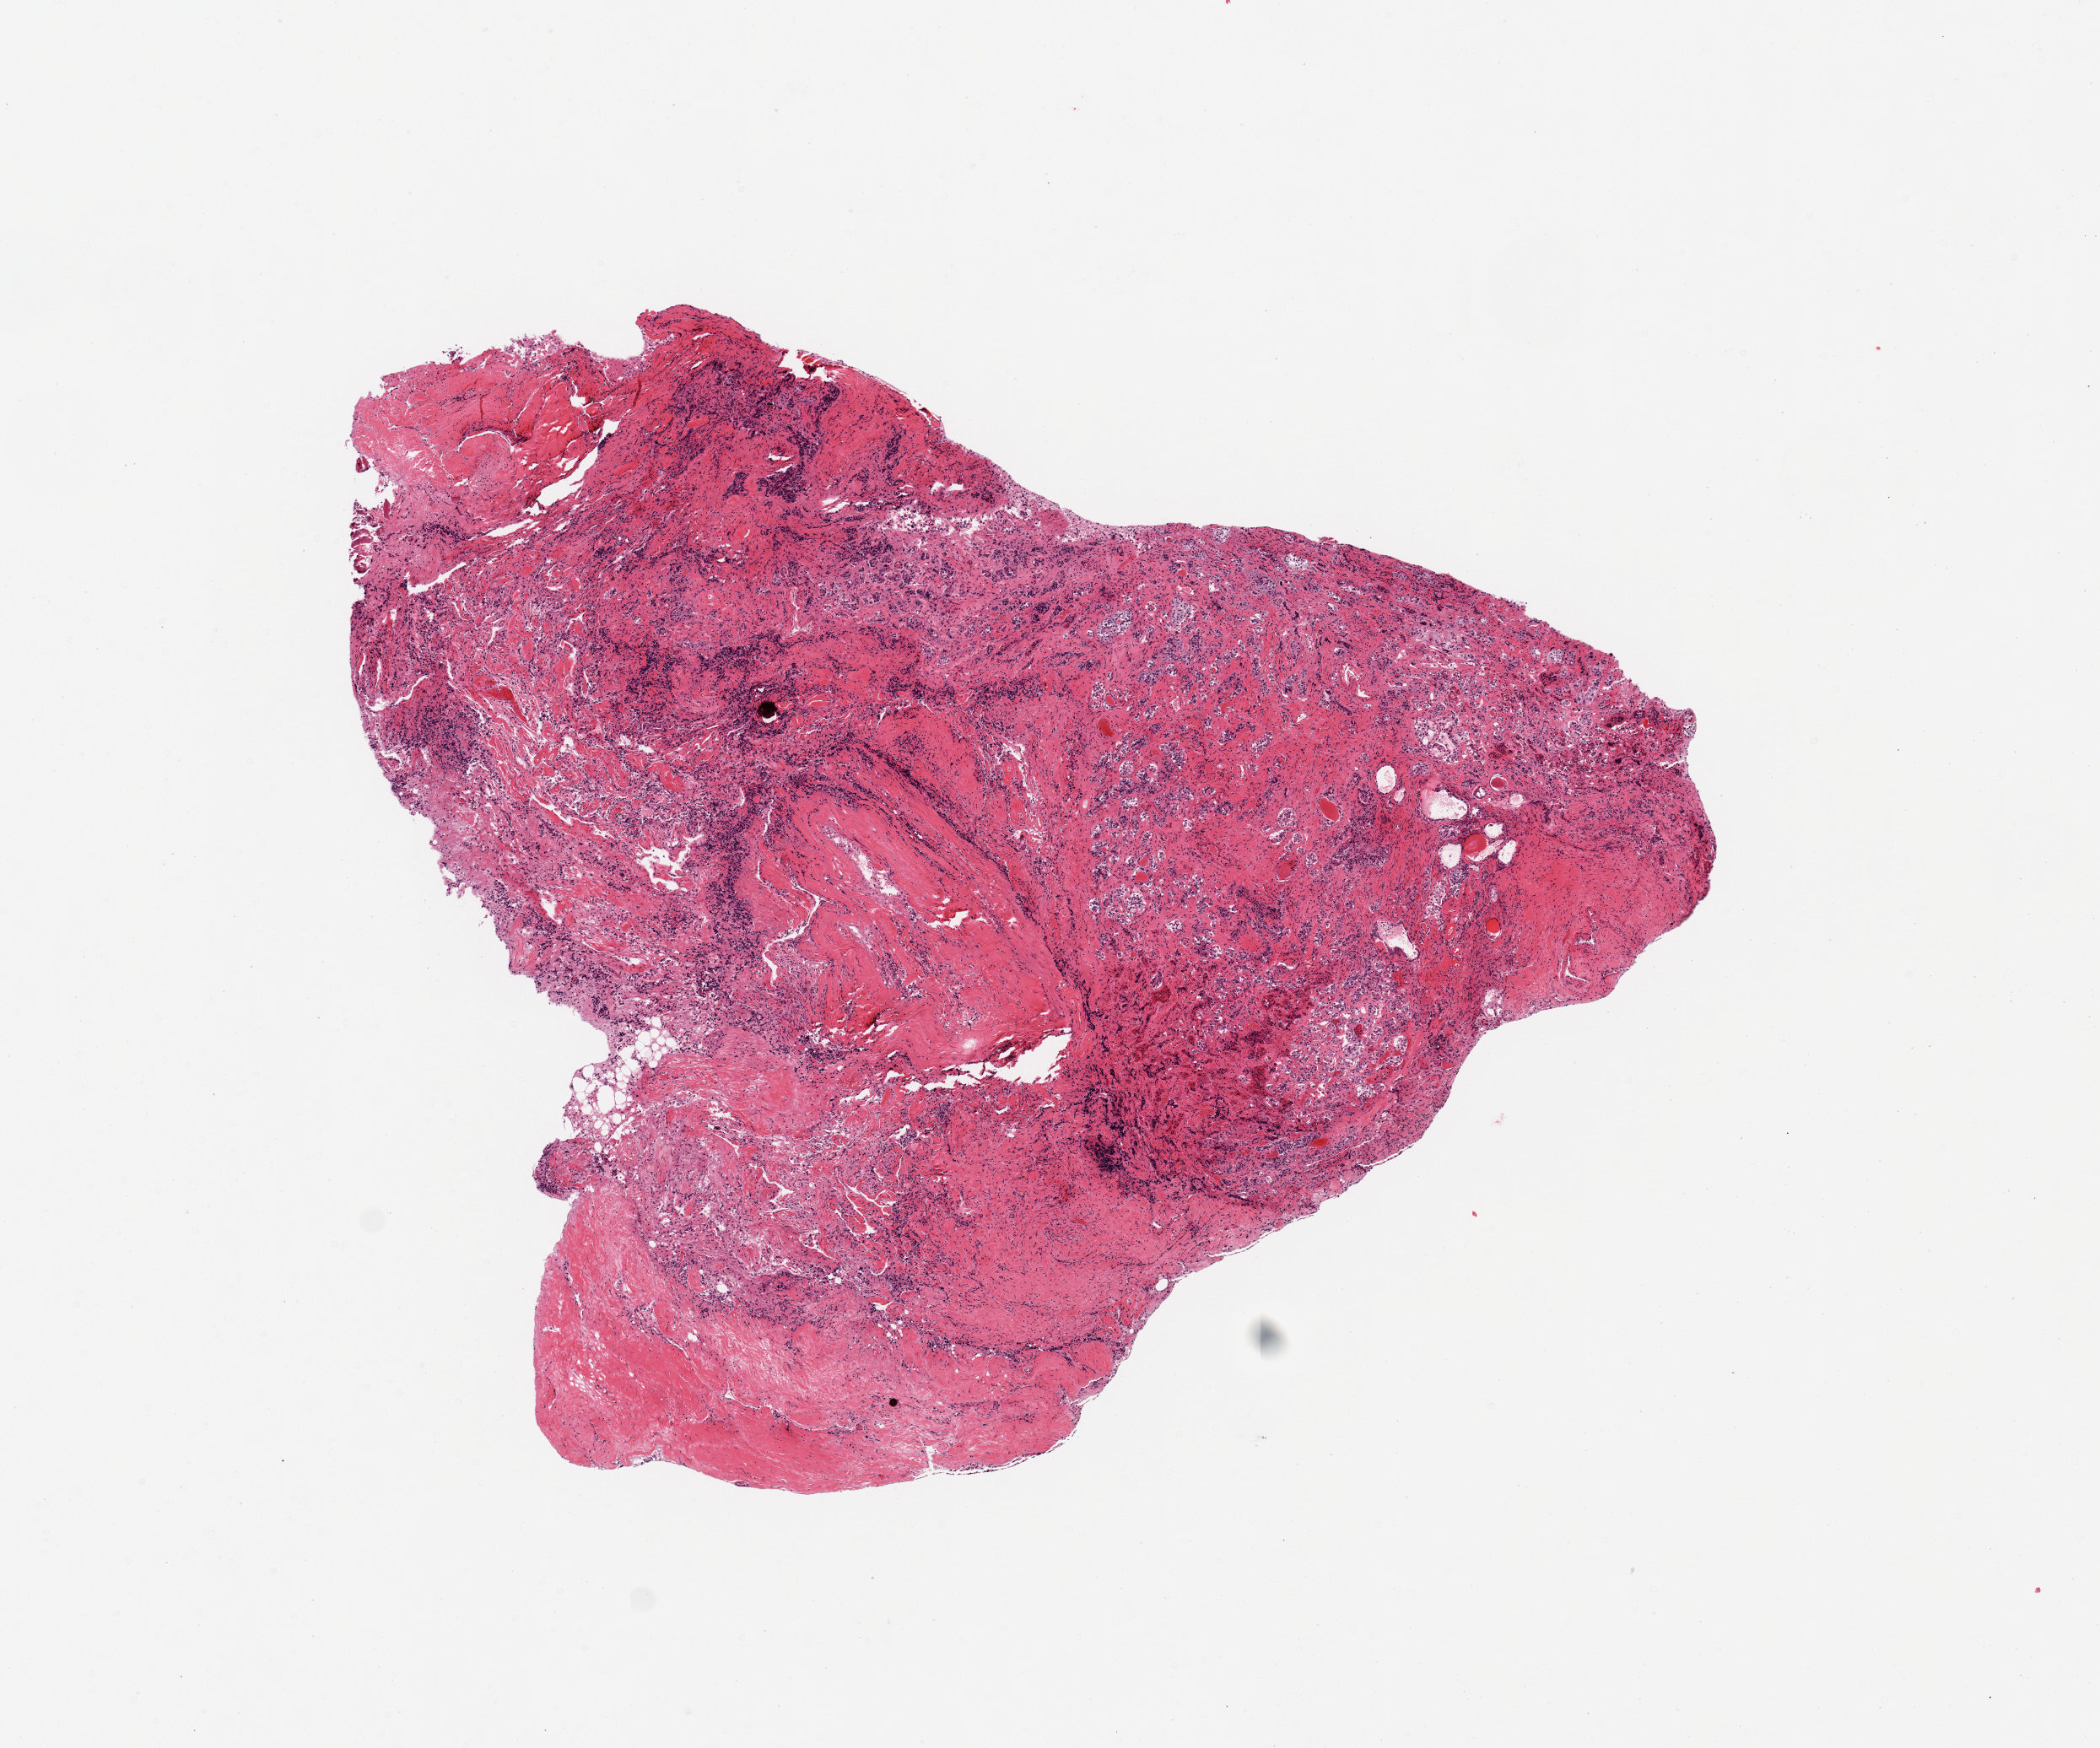
Digitized hematoxylin and eosin (H&E)-stained section, shown as a low-resolution overview of the whole scanned area (about 9.8 x 8.2 mm, acquisition: 20x scan), PAXgene-fixed paraffin-embedded (PFPE) section, sampled site (target tissue): pituitary, donor tissue sample. Male donor.
Review note (as recorded): 1 piece; adenohypophysis, dura.